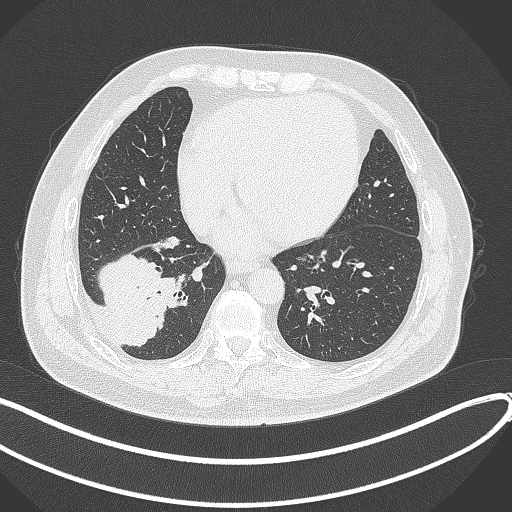
Chest CT, one axial slice; position 122 of 360 along the scan axis; lung window (W 1500 / L -600 HU); 1 mm slice thickness; 512 × 512 image matrix, field of view 400 × 400 mm. Patient: male, 59 years.
Structures marked on this image (rectangle marked by the reading radiologist):
- lung tumour (recorded histology: adenocarcinoma): bounding box [x1, y1, x2, y2] px = [91, 376, 212, 440]
- lung tumour (recorded histology: adenocarcinoma): [95, 248, 185, 350]